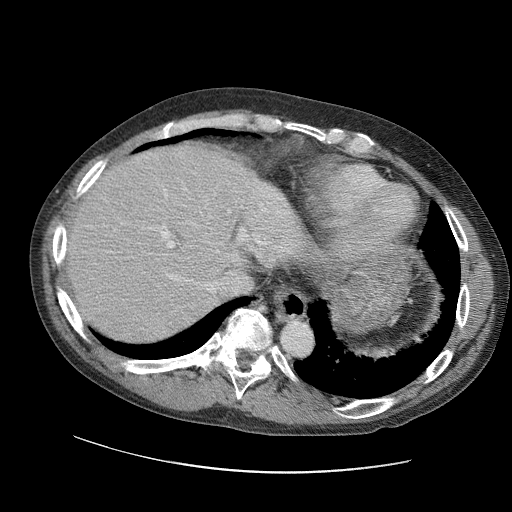
Contrast-enhanced abdominal CT (liver protocol), one axial slice; slice 81 of 109 in the series (ordered by position); reconstruction kernel STANDARD; 120 kVp; soft-tissue window (W 400 / L 40 HU); 512 × 512 image matrix, field of view 400 × 400 mm. From the clinical record (not read from this slice): diagnosis: hepatocellular carcinoma (patient treated with transarterial chemoembolisation; whether this scan precedes or follows treatment is not stated here); TNM stage (as recorded): Stage-IIIC; Child-Pugh class: B; tumour differentiation: well differentiated; tumour nodularity: uninodular.
Structures marked on this image (semi-automatic segmentation, software-assisted and operator-edited):
- abdominal aorta: bounding box [x1, y1, x2, y2] px = [282, 321, 313, 354]
- liver parenchyma outside the tumour (the mass and vessels are separate outlines, so this box may not span the whole liver): [62, 140, 314, 342]
- liver vessels: [111, 171, 307, 325]